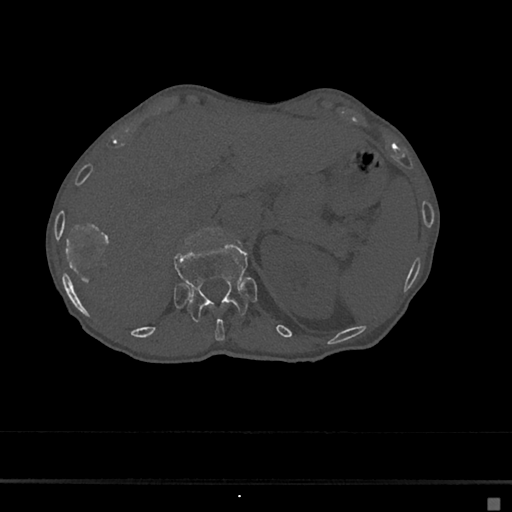
CT including the spine, one axial slice. Position 131 of 797 along the scan axis. 120 kVp. Bone window (W 1800 / L 400 HU). 0.5 mm slice thickness. 512 × 512 image matrix, field of view 360 × 360 mm. Patient: female, 68 years. From the clinical record (not read from this slice): primary cancer: renal.
Structures marked on this image (semi-automatically segmented with operator editing):
- T11 vertebra: box from (x=215, y=318) to (x=225, y=341) px
- T12 vertebra: (x=173, y=243)–(x=248, y=322)